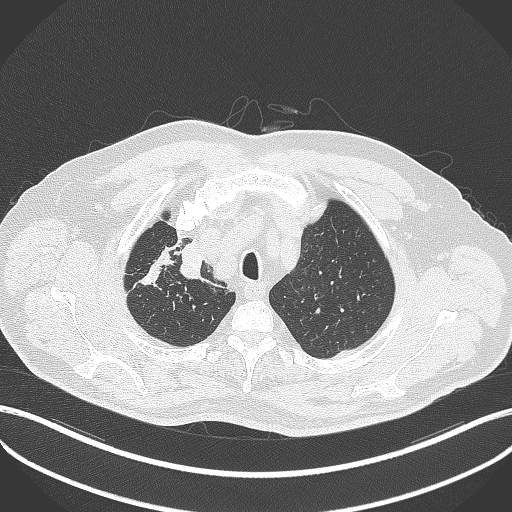
Chest CT, one axial slice. Position 327 of 411 along the scan axis. Reconstruction kernel B70f. Lung window (W 1500 / L -600 HU). 512 × 512 image matrix. Patient: male, 60 years. From the clinical record (not read from this slice): clinical TNM (as recorded): T1b N1 M0.
Outlined on this slice (bounding box drawn by a radiologist):
- lung tumour (recorded histology: squamous cell carcinoma): bounding box (x1, y1, x2, y2) in pixels: (176, 236, 208, 281)